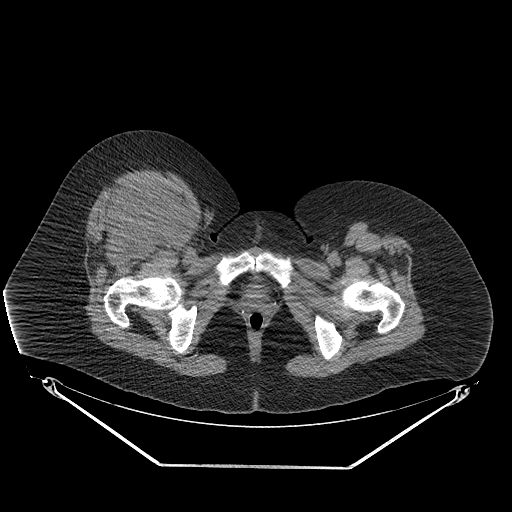
CT of an extremity soft-tissue mass (from a PET/CT study), one axial slice. Reconstruction kernel STANDARD. Soft-tissue window (W 400 / L 40 HU). 3.75 mm slice thickness. 512 × 512 image matrix, field of view 500 × 500 mm. Female patient. Case-level facts recorded for this patient, not image findings: histological type: malignant solitary fibrous tumor; grade: intermediate; site of the primary tumour: right thigh.
Structures marked on this image (expert contour drawn on MRI and transferred to this co-registered scan by the dataset authors):
- gross tumour volume including surrounding oedema: box from (x=100, y=181) to (x=177, y=243) px
- gross tumour volume (mass): (x=103, y=185)–(x=177, y=238)